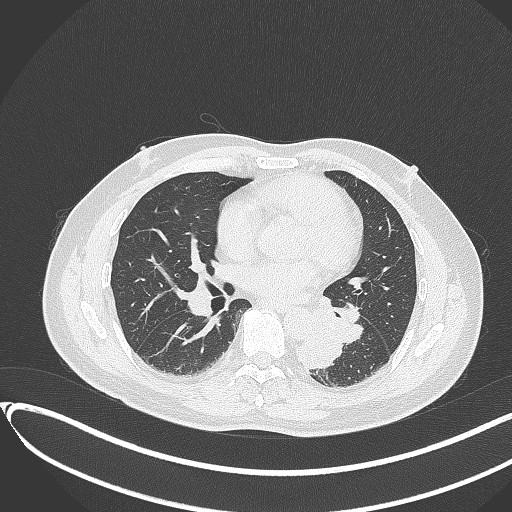
Chest CT, one axial slice. Slice 164 of 417 in the series (ordered by position). Reconstruction kernel B70f. 120 kVp. Lung window (W 1500 / L -600 HU). 1 mm slice thickness. 512 × 512 image matrix, field of view 400 × 400 mm. Patient: male, 54 years. Case-level facts recorded for this patient, not image findings: clinical TNM (as recorded): T3 N0 M0.
Outlined on this slice (rectangle marked by the reading radiologist):
- lung tumour (recorded histology: squamous cell carcinoma): bounding box <295,323,348,372> (left, top, right, bottom; pixels)